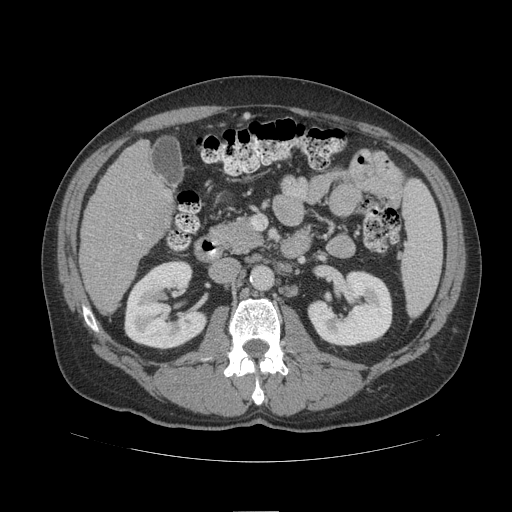
Contrast-enhanced abdominal CT (liver protocol), one axial slice; slice 45 of 109 in the series (ordered by position); reconstruction kernel STANDARD; 140 kVp; soft-tissue window (W 400 / L 40 HU); 2.5 mm slice thickness; 512 × 512 image matrix, field of view 420 × 420 mm. Case-level facts recorded for this patient, not image findings: diagnosis: hepatocellular carcinoma (patient treated with transarterial chemoembolisation; whether this scan precedes or follows treatment is not stated here); TNM stage (as recorded): Stage-IIIB; Child-Pugh class: A; tumour differentiation: poorly differentiated.
Outlined on this slice (semi-automatic segmentation, software-assisted and operator-edited):
- liver parenchyma outside the tumour (the mass and vessels are separate outlines, so this box may not span the whole liver): box from (x=80, y=140) to (x=172, y=314) px
- liver vessels: (x=139, y=235)–(x=142, y=239)